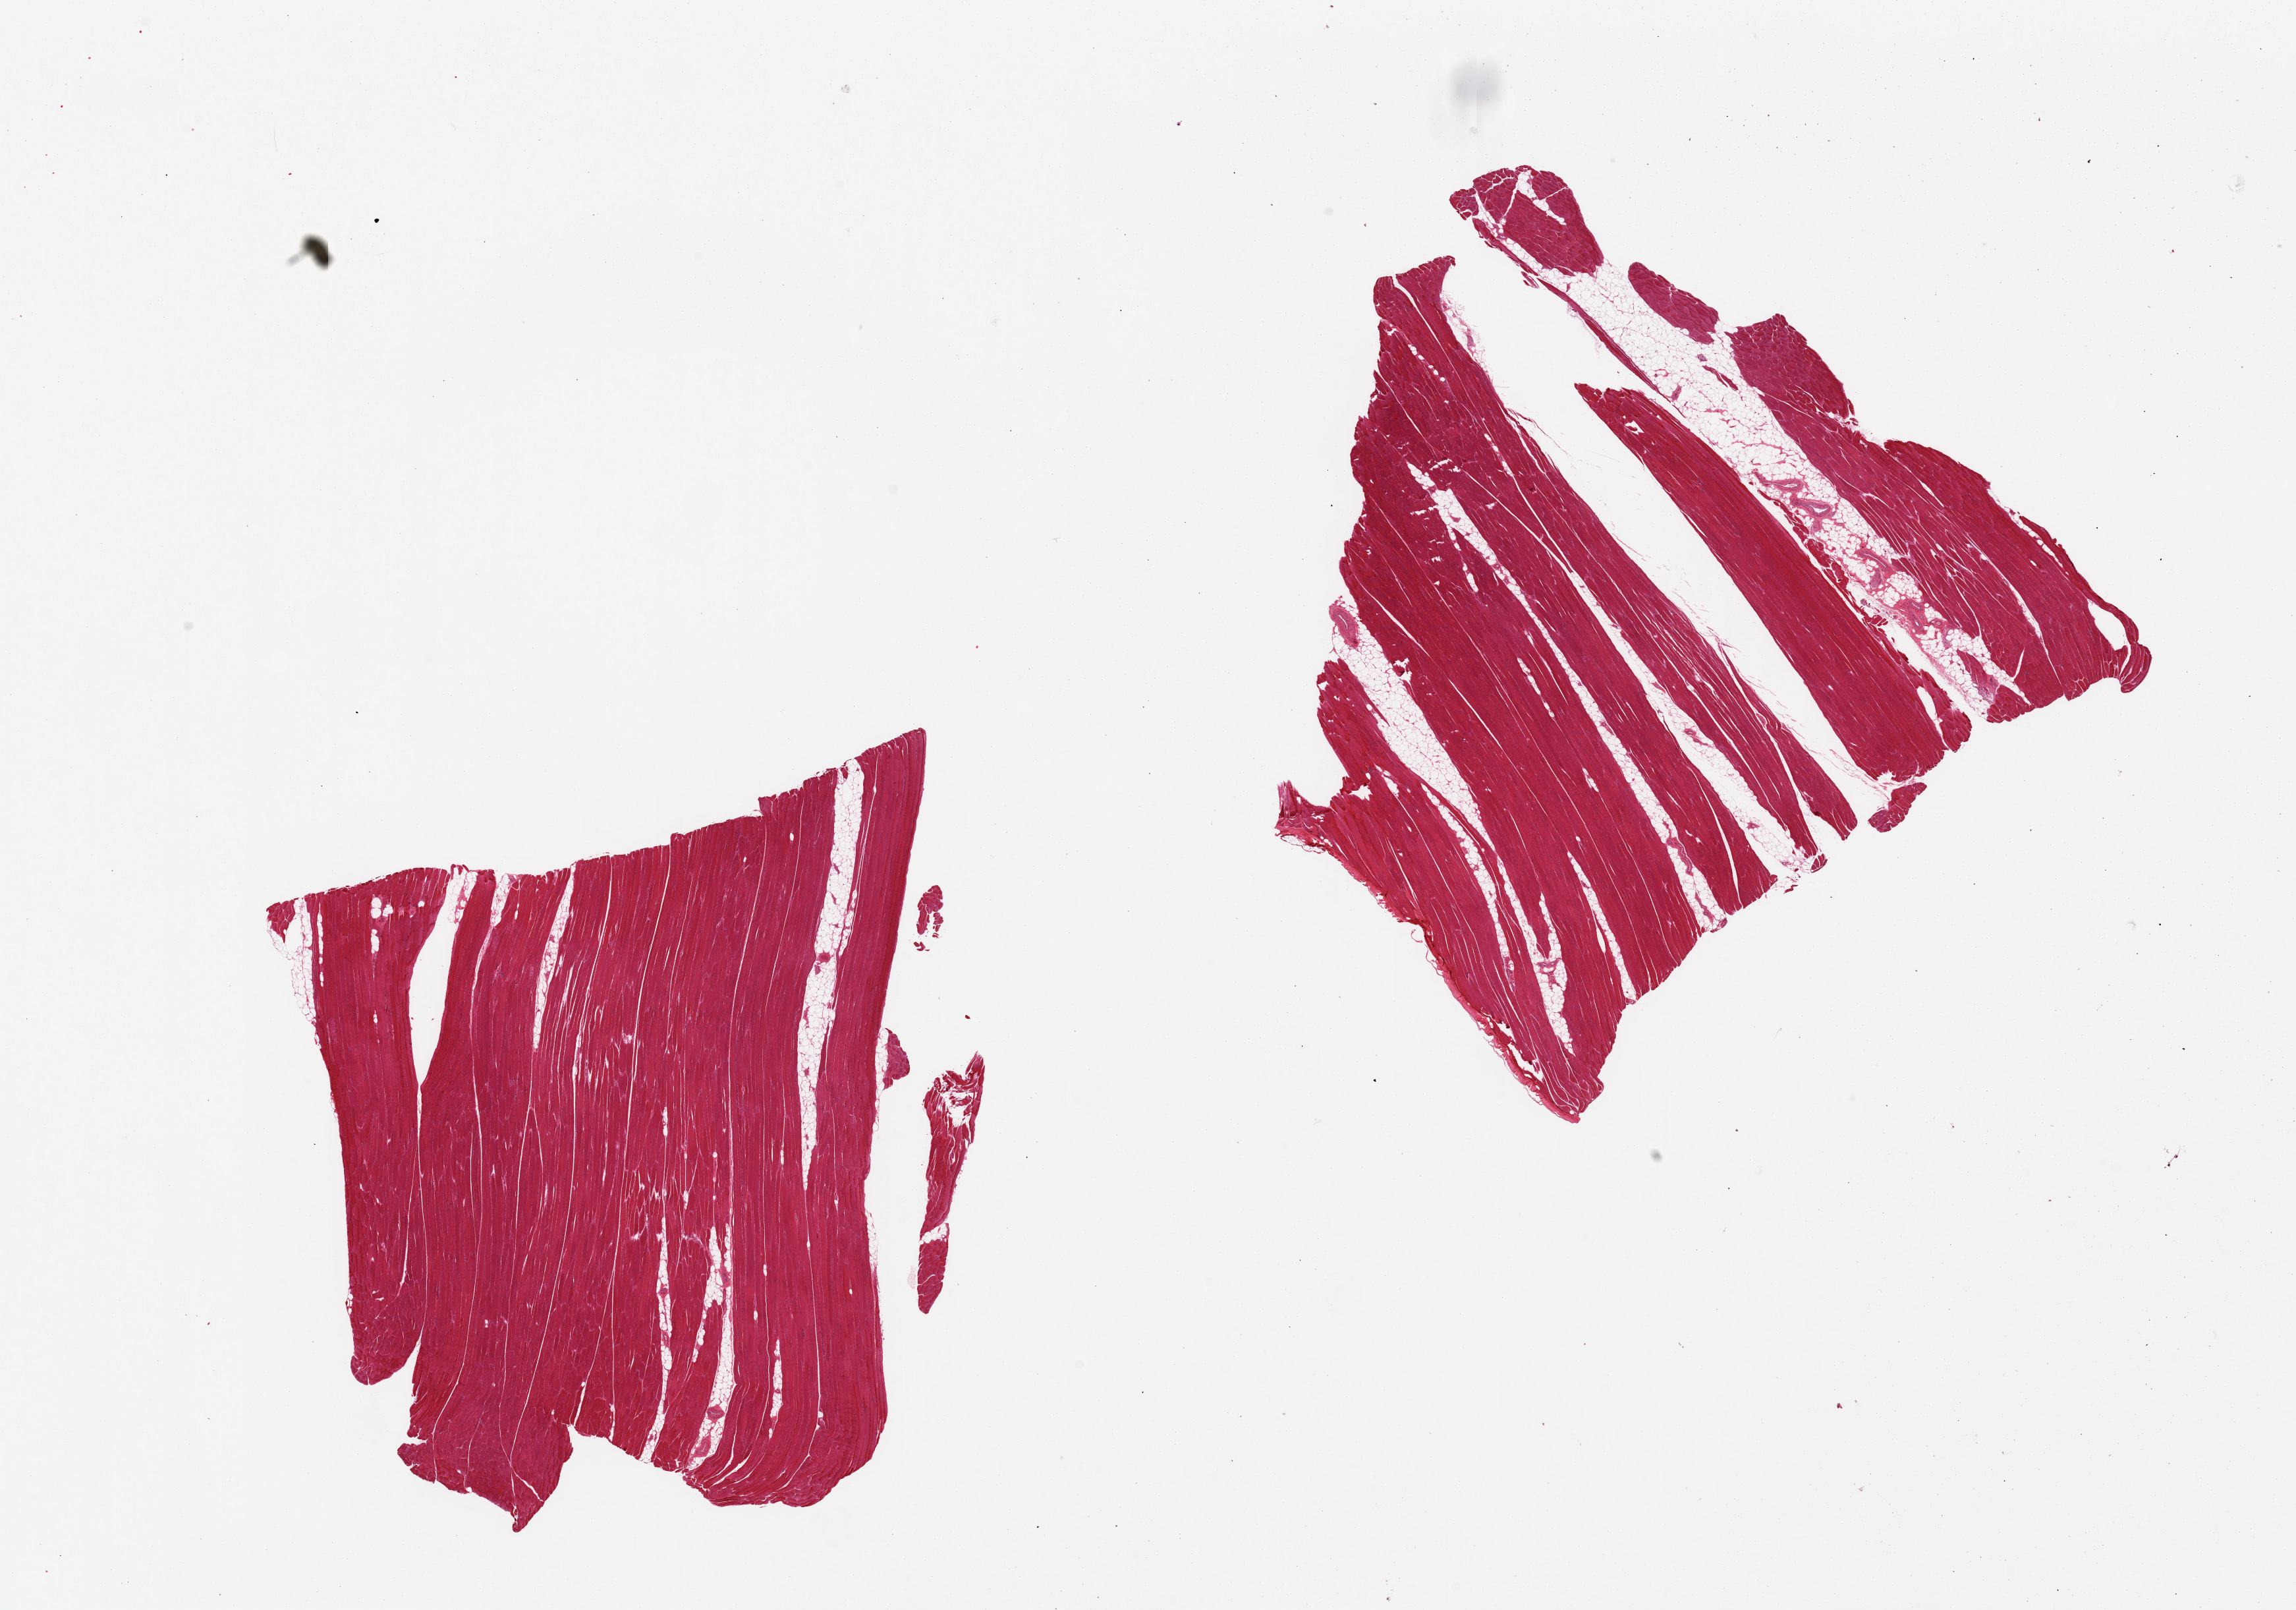
Haematoxylin and eosin whole-slide image, low-resolution overview of the scanned area, about 27.6 x 19.3 mm (acquisition: 20x scan), PAXgene-fixed paraffin-embedded (PFPE) section, target tissue: skeletal muscle, tissue donor sample. Donor: female.
Pathologist's review note for this sample: 2 pieces, ~10% interstitial fat.